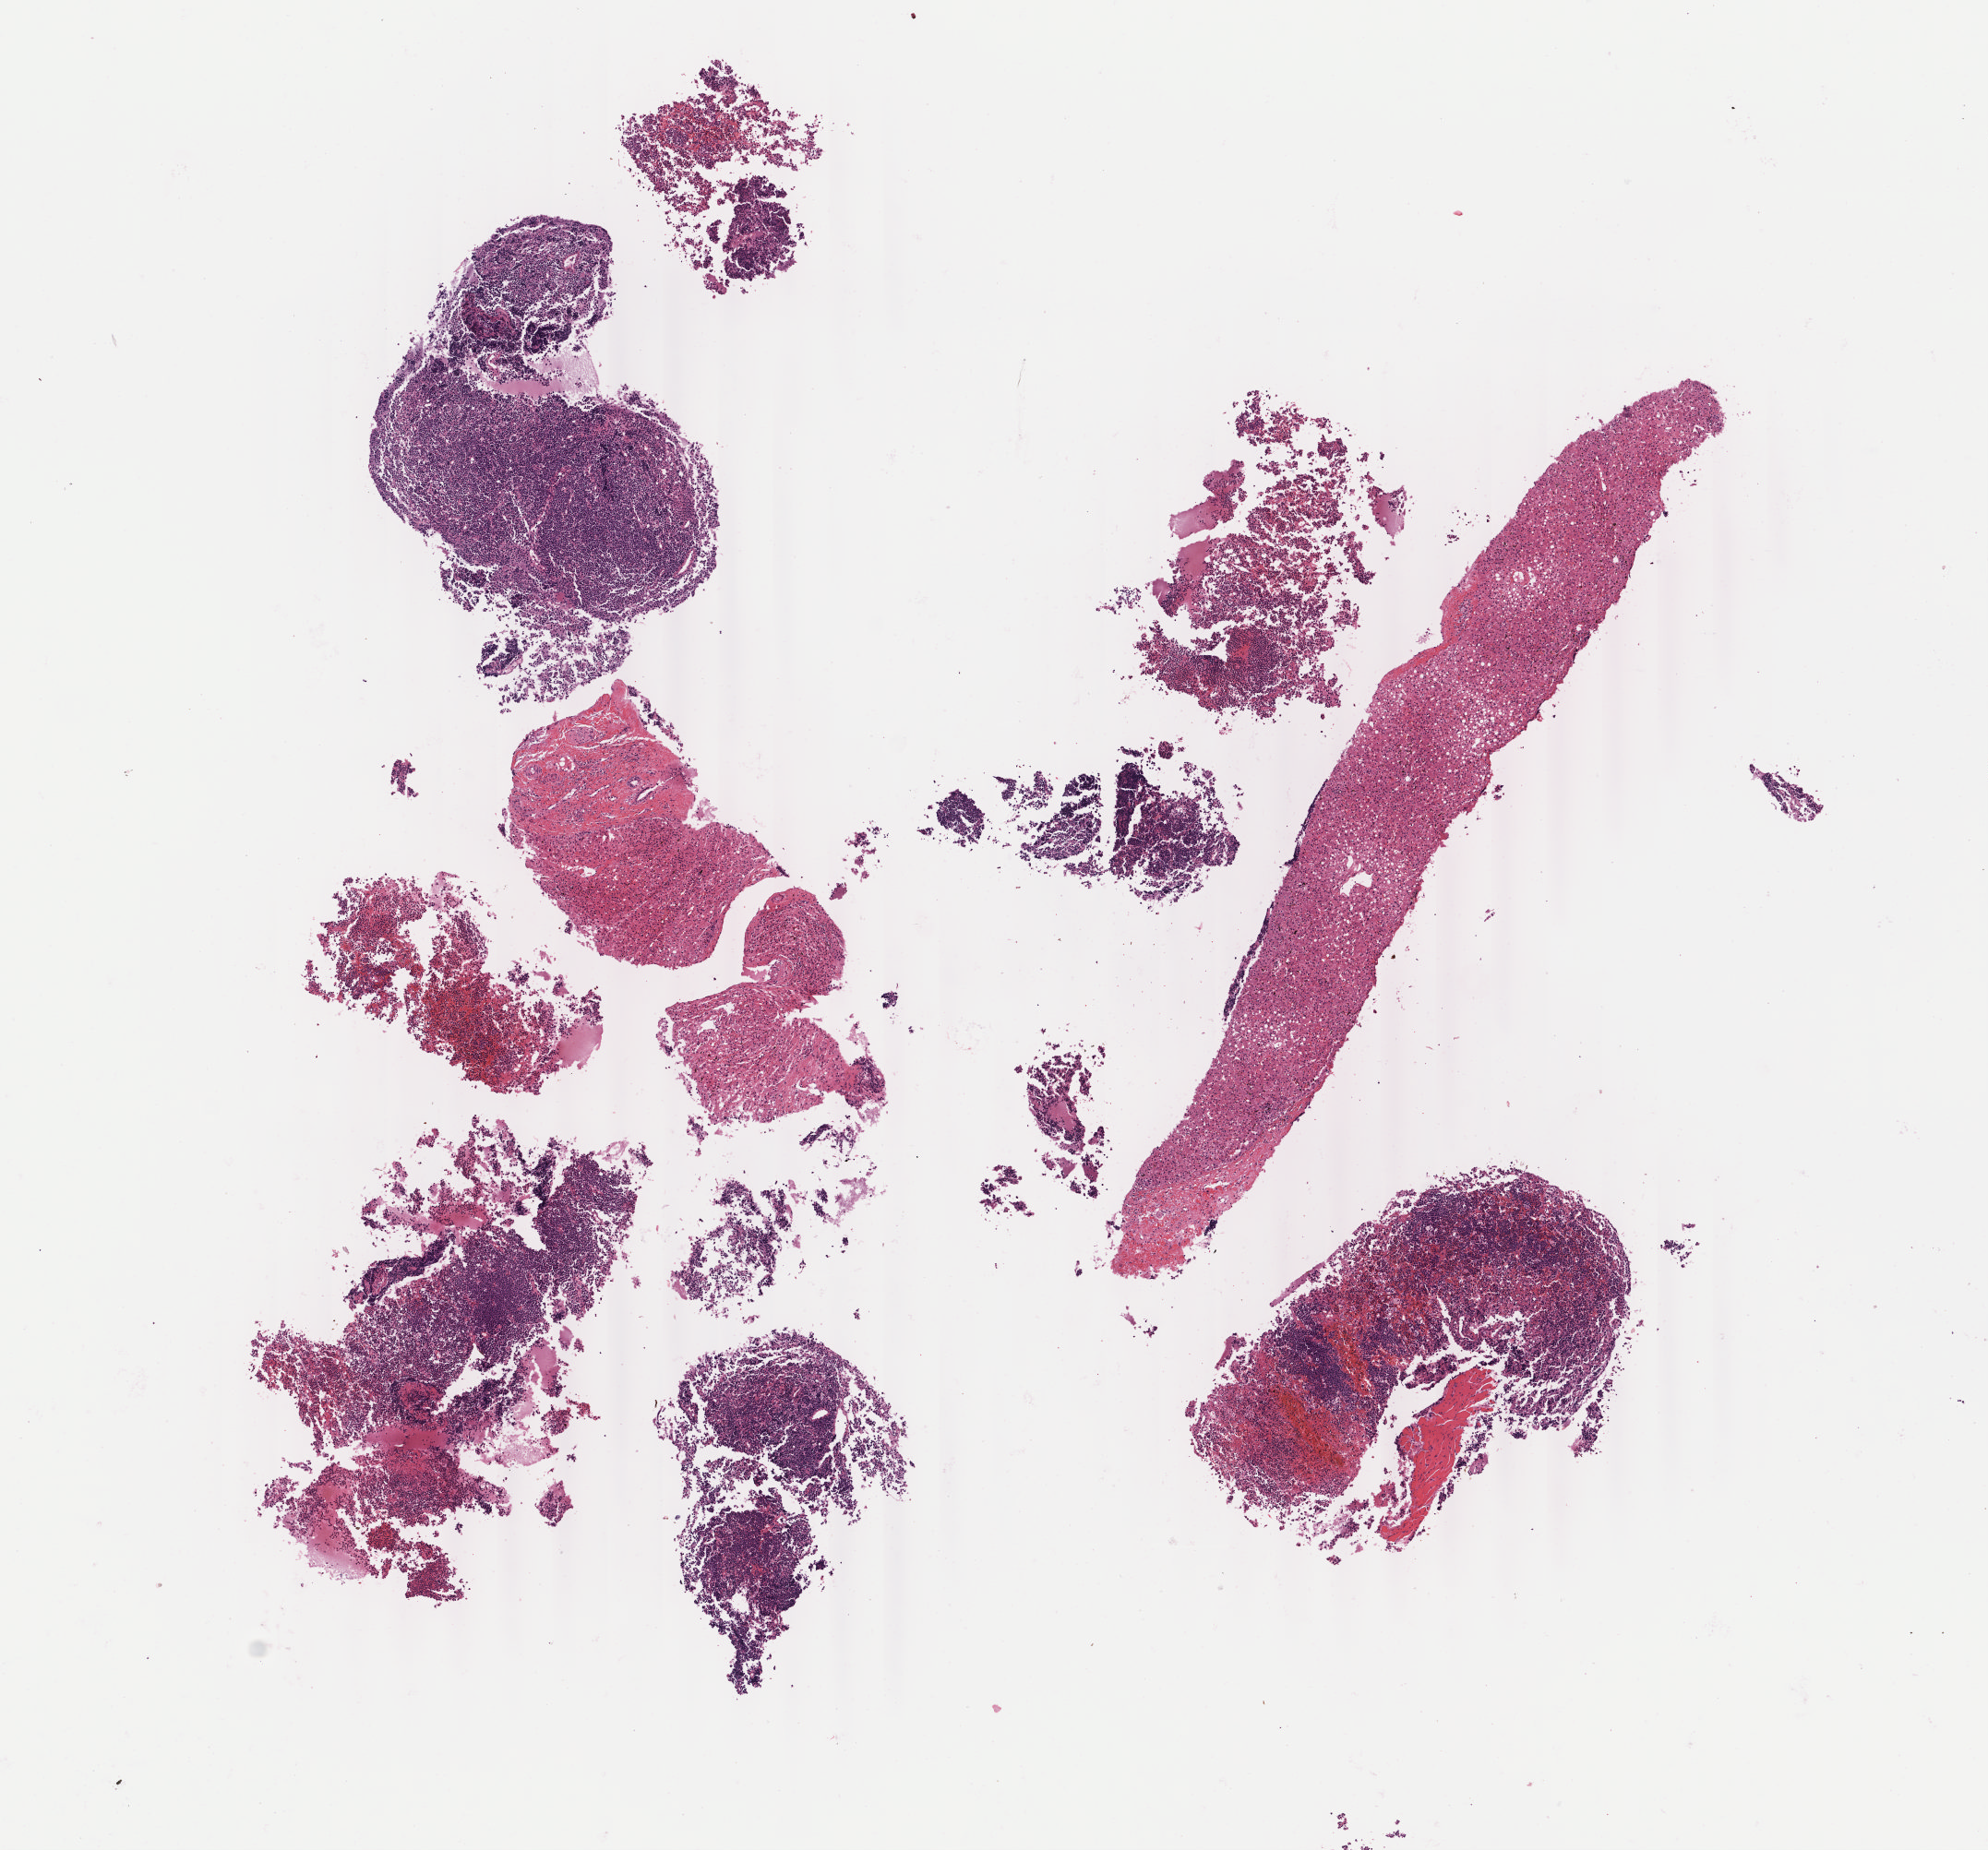
H&E whole-slide image — shown as a low-resolution overview of the whole scanned area (about 8.6 x 8.0 mm). Formalin-fixed, paraffin-embedded (FFPE) tissue. Primary tumor. Site: liver. Patient: male, age at initial diagnosis 5 years. Pathologist review of this section (percent, as recorded): tumor cells 60%, tumor nuclei 85%, stromal cells 30%, necrosis 10%, normal cells 0%. Inflammatory infiltration, as recorded: lymphocyte infiltration 20%, monocyte infiltration 30%, neutrophil infiltration 5%.
Ann Arbor stage (patient): Stage III. Histologic diagnosis: Burkitt lymphoma, NOS.